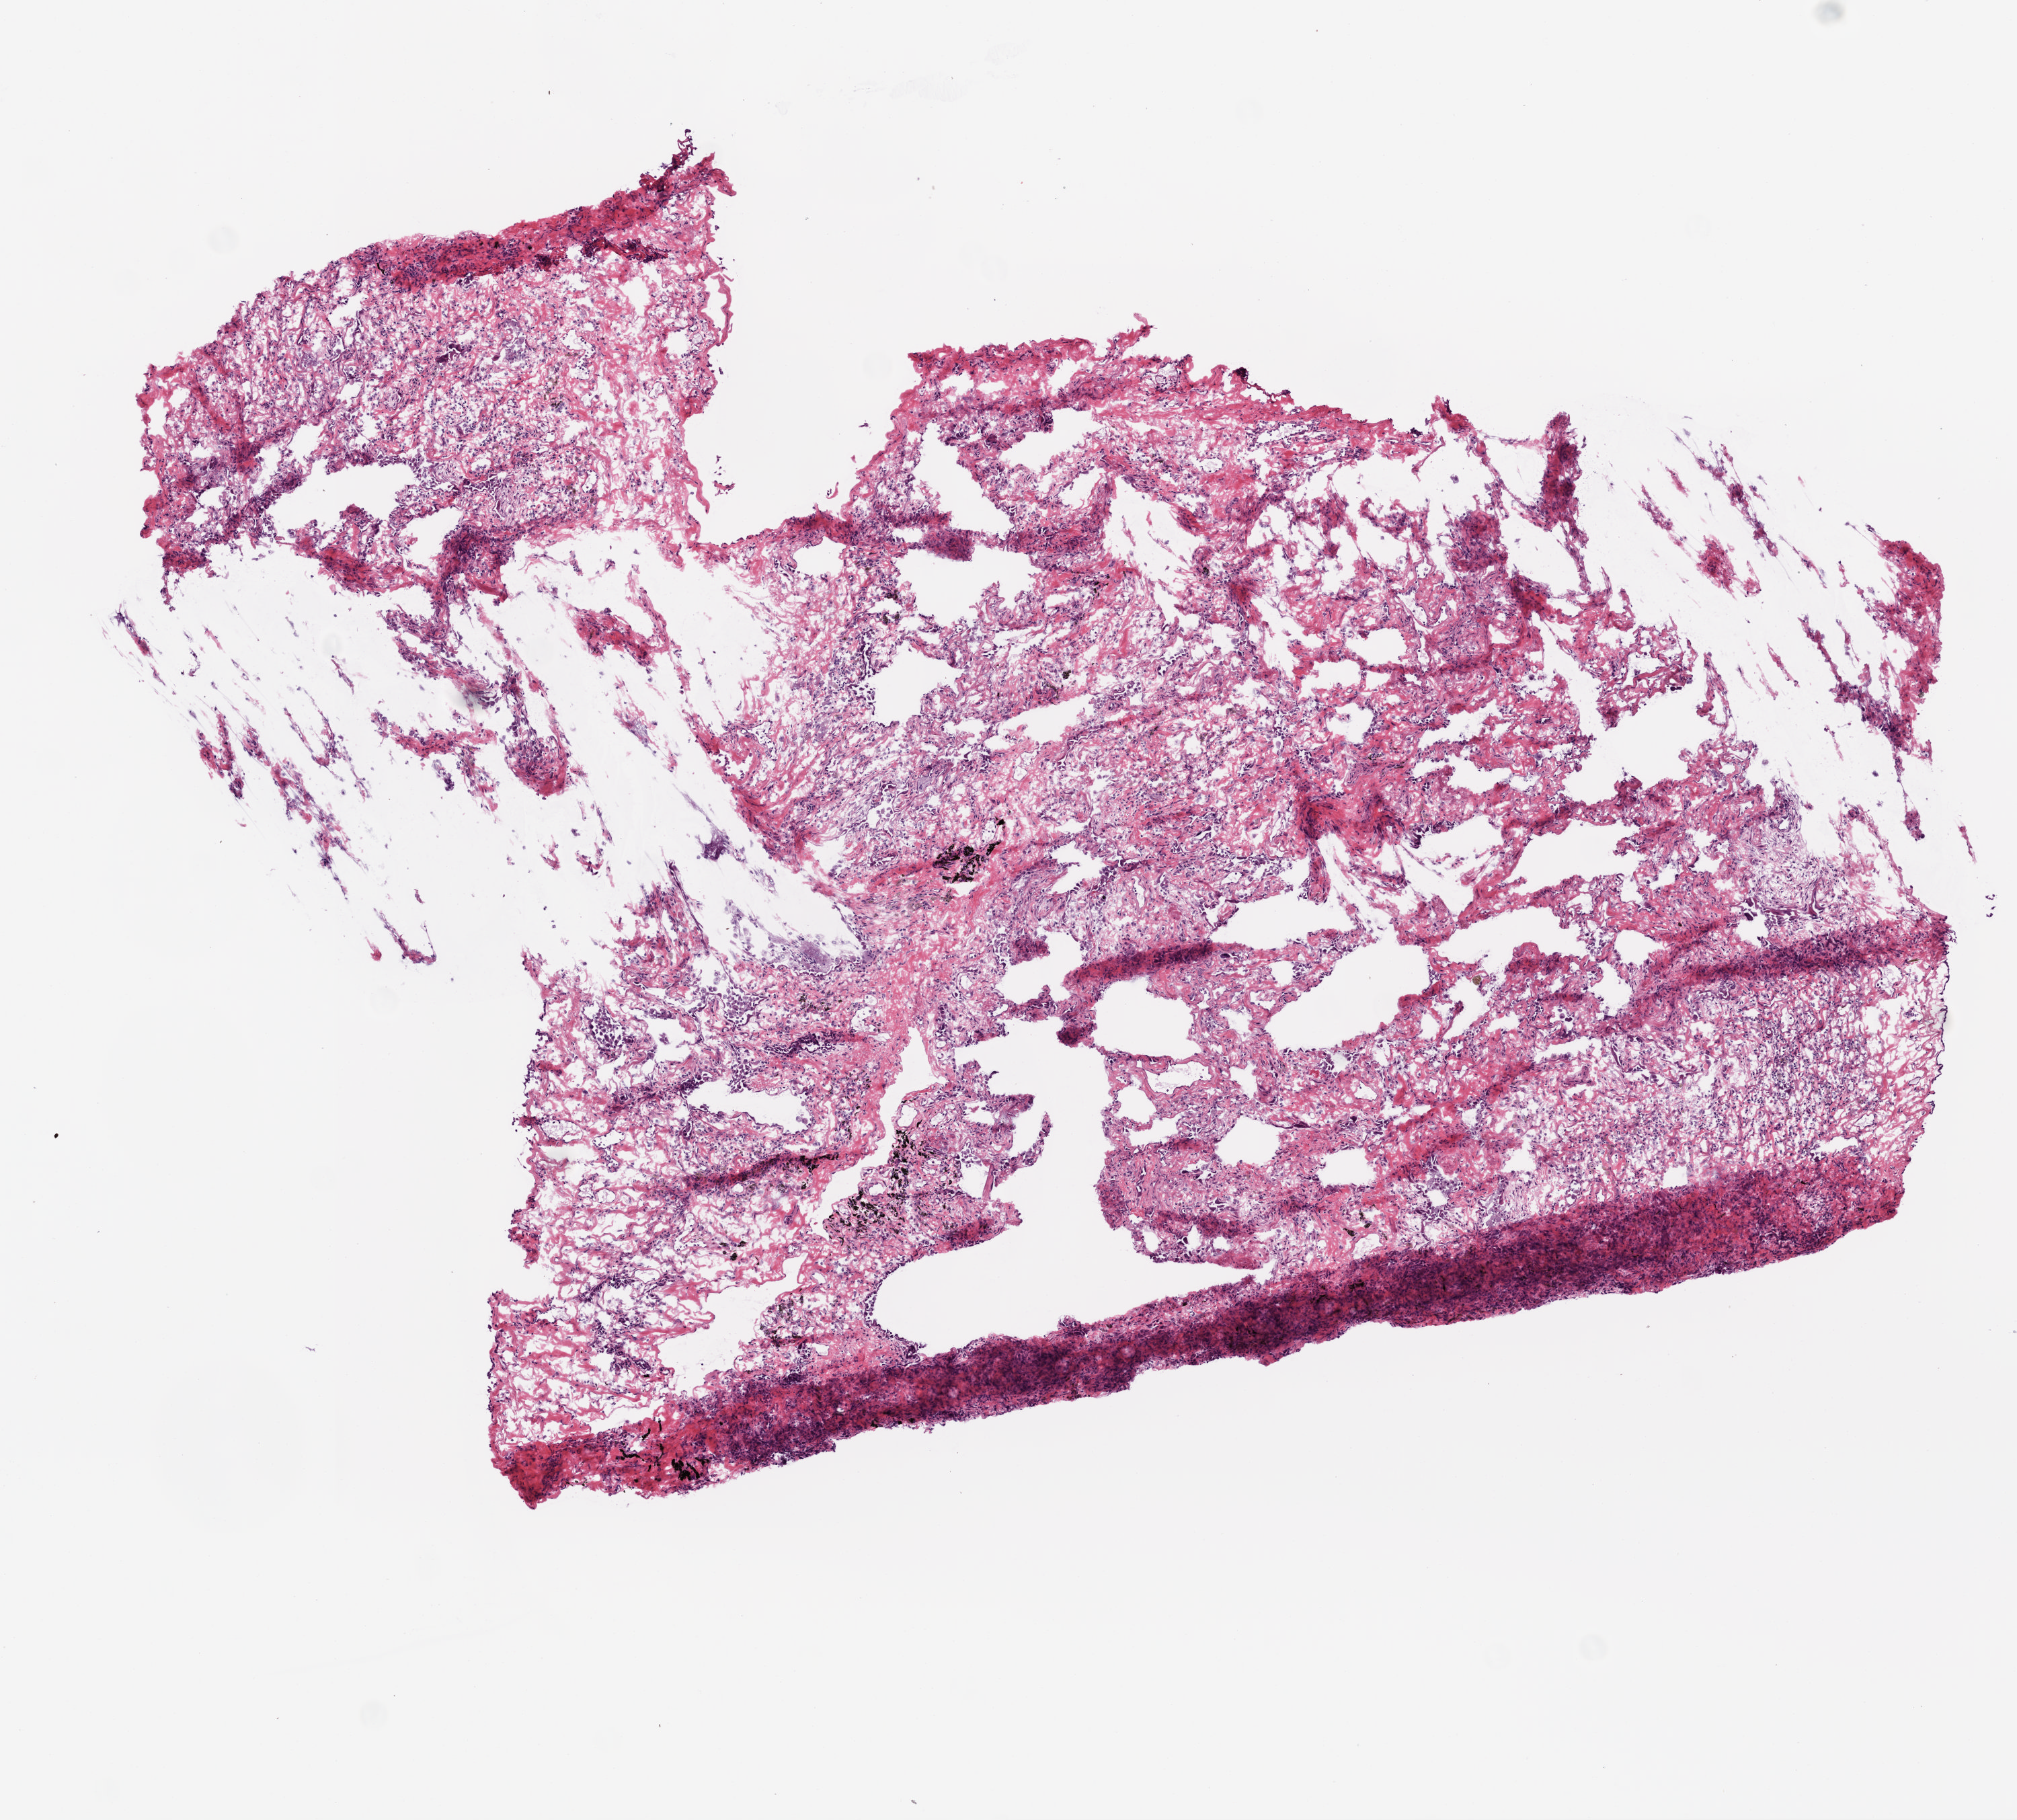
Digitized H&E-stained tissue section (whole slide) — shown as a low-resolution overview of the whole scanned area (about 6.0 x 5.4 mm), frozen section from the top of the tissue portion, sample: solid tissue normal (non-tumour tissue), lung. Patient: female, age at initial diagnosis 62 years.
This section: solid tissue normal sample (biorepository sample class). Patient diagnosis: Squamous cell carcinoma, NOS (lower lobe, lung).